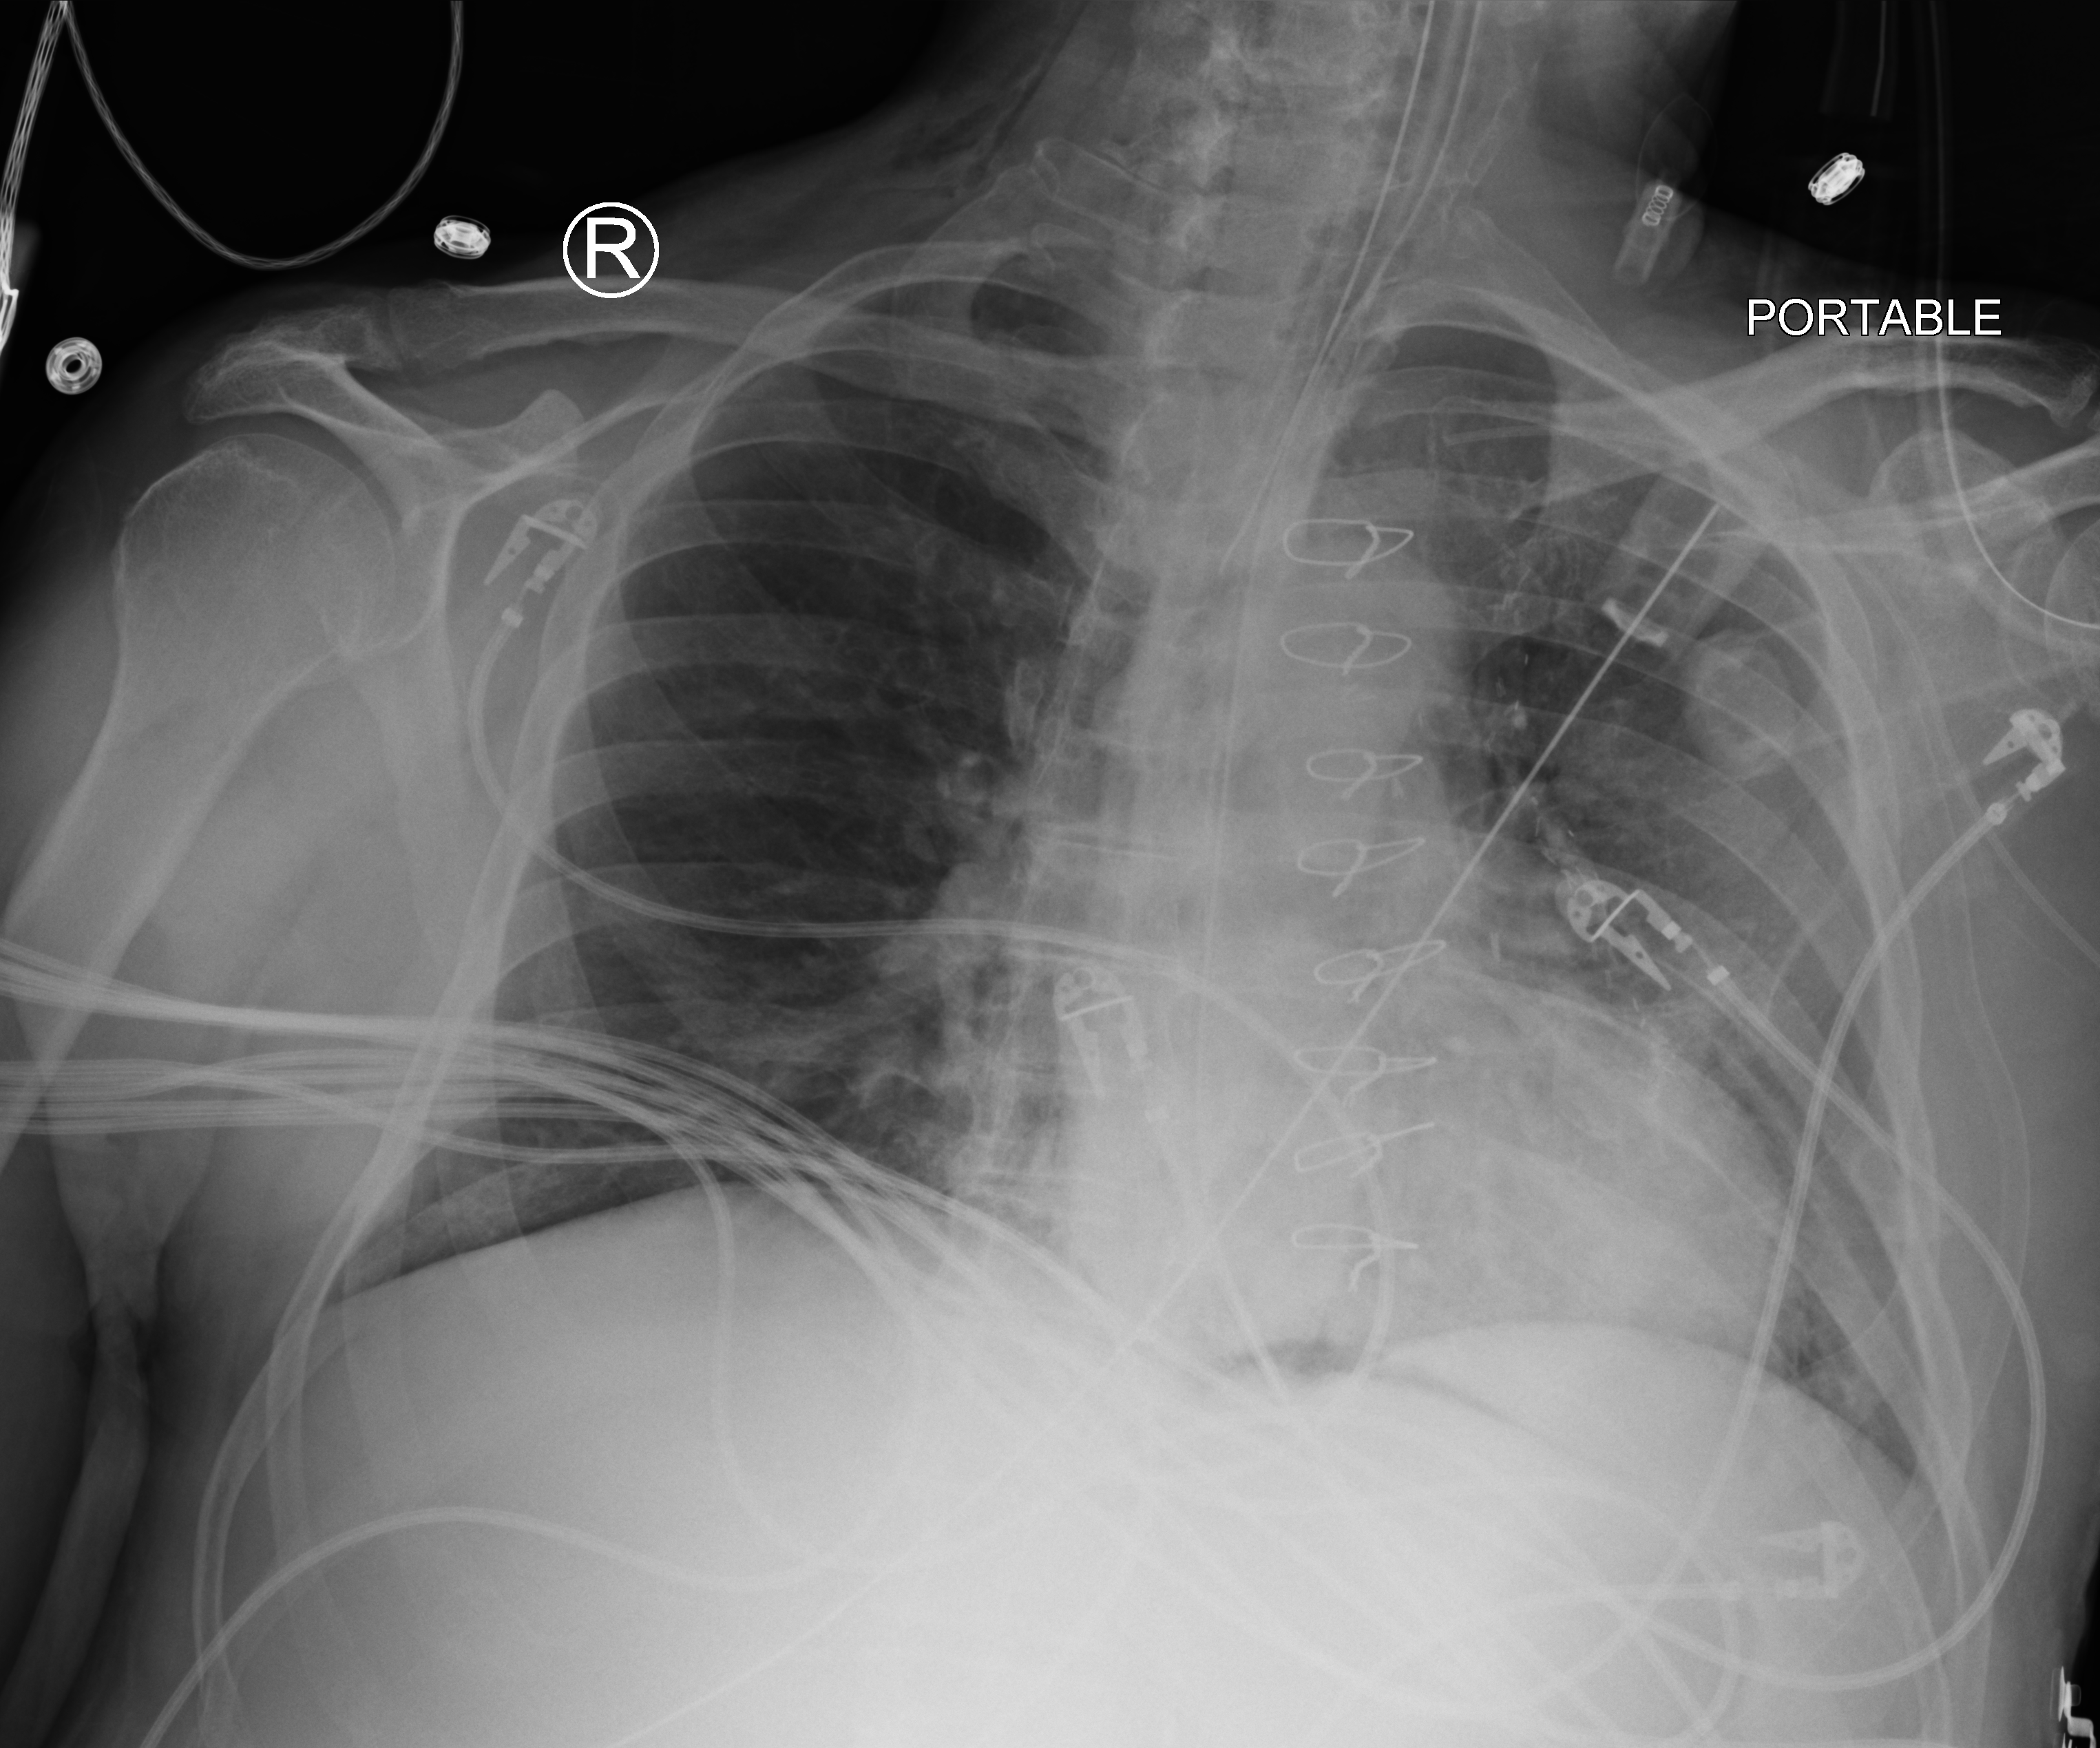
Bedside chest radiograph (computed radiography); anteroposterior (AP) projection. Male patient hospitalised with COVID-19, age 60–74 years.
Hospital-stay facts (about this admission, not read from this image; timing relative to this image not recorded): mechanically ventilated during this hospital stay: yes; length of hospital stay: 22 days.